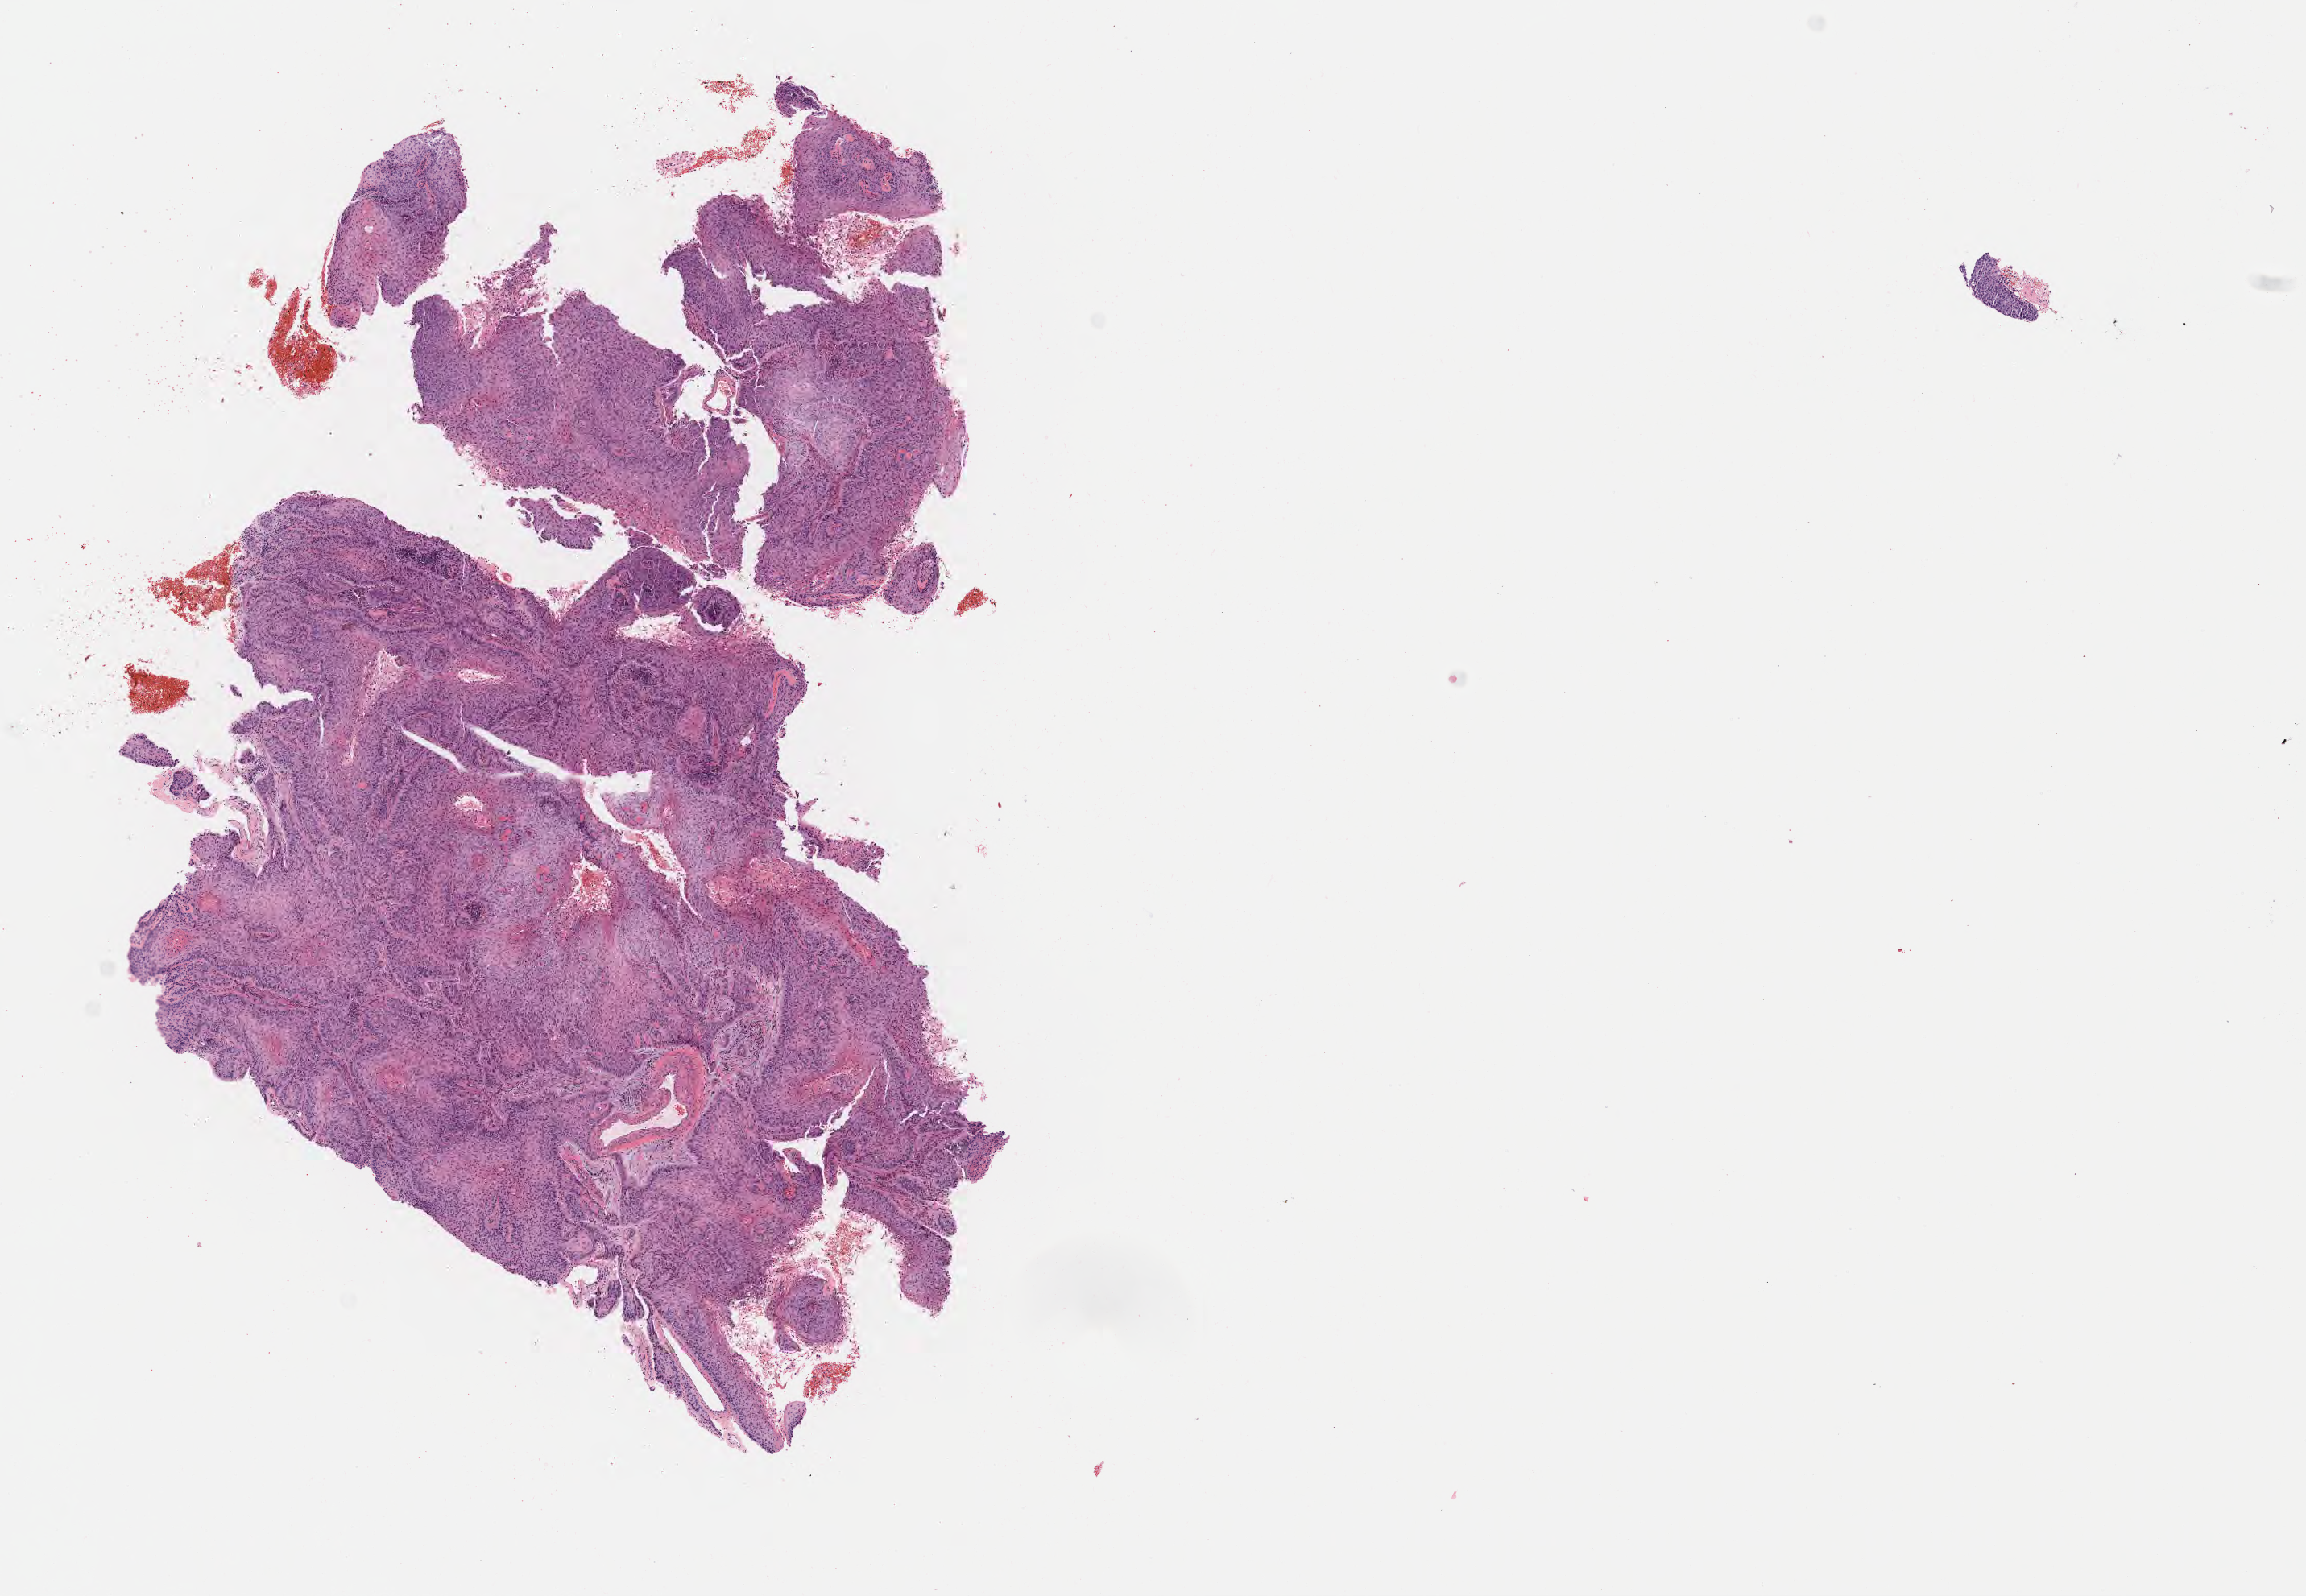
H&E whole-slide image — low-resolution overview of the scanned area, about 11.6 x 8.0 mm. Specimen: tumor tissue. Site: cervix. Patient female; aged 46.
Histologic diagnosis: Squamous cell carcinoma, keratinizing, NOS.